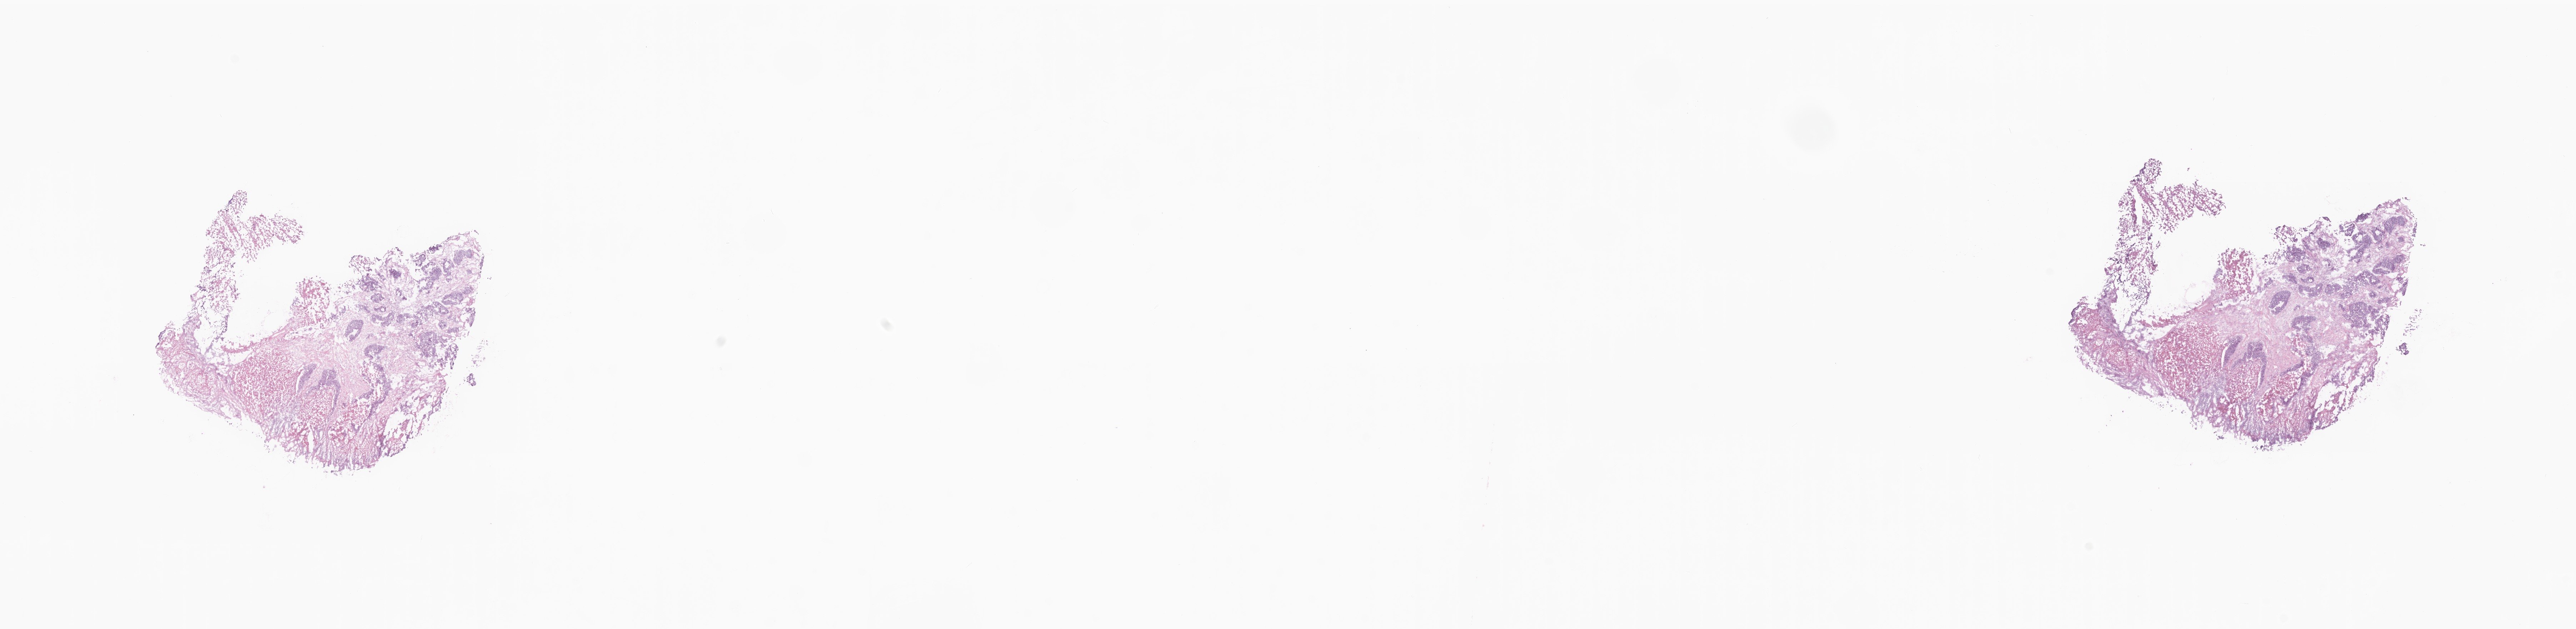
Digitized H&E-stained section, low-resolution overview of the scanned area, about 30.4 x 7.4 mm, frozen section (tissue freezing medium), primary tumor, site: ascending colon. Male patient; age at initial diagnosis 76 years. Slide review estimates, as recorded: tumor cells 19%, tumor nuclei 50%, stromal cells 22%, necrosis 40%, normal cells 19%. Inflammatory infiltration, as recorded: lymphocyte infiltration 1%, monocyte infiltration 5%, neutrophil infiltration 1%.
Section: top of the tissue portion. Histologic diagnosis: Adenocarcinoma, NOS.